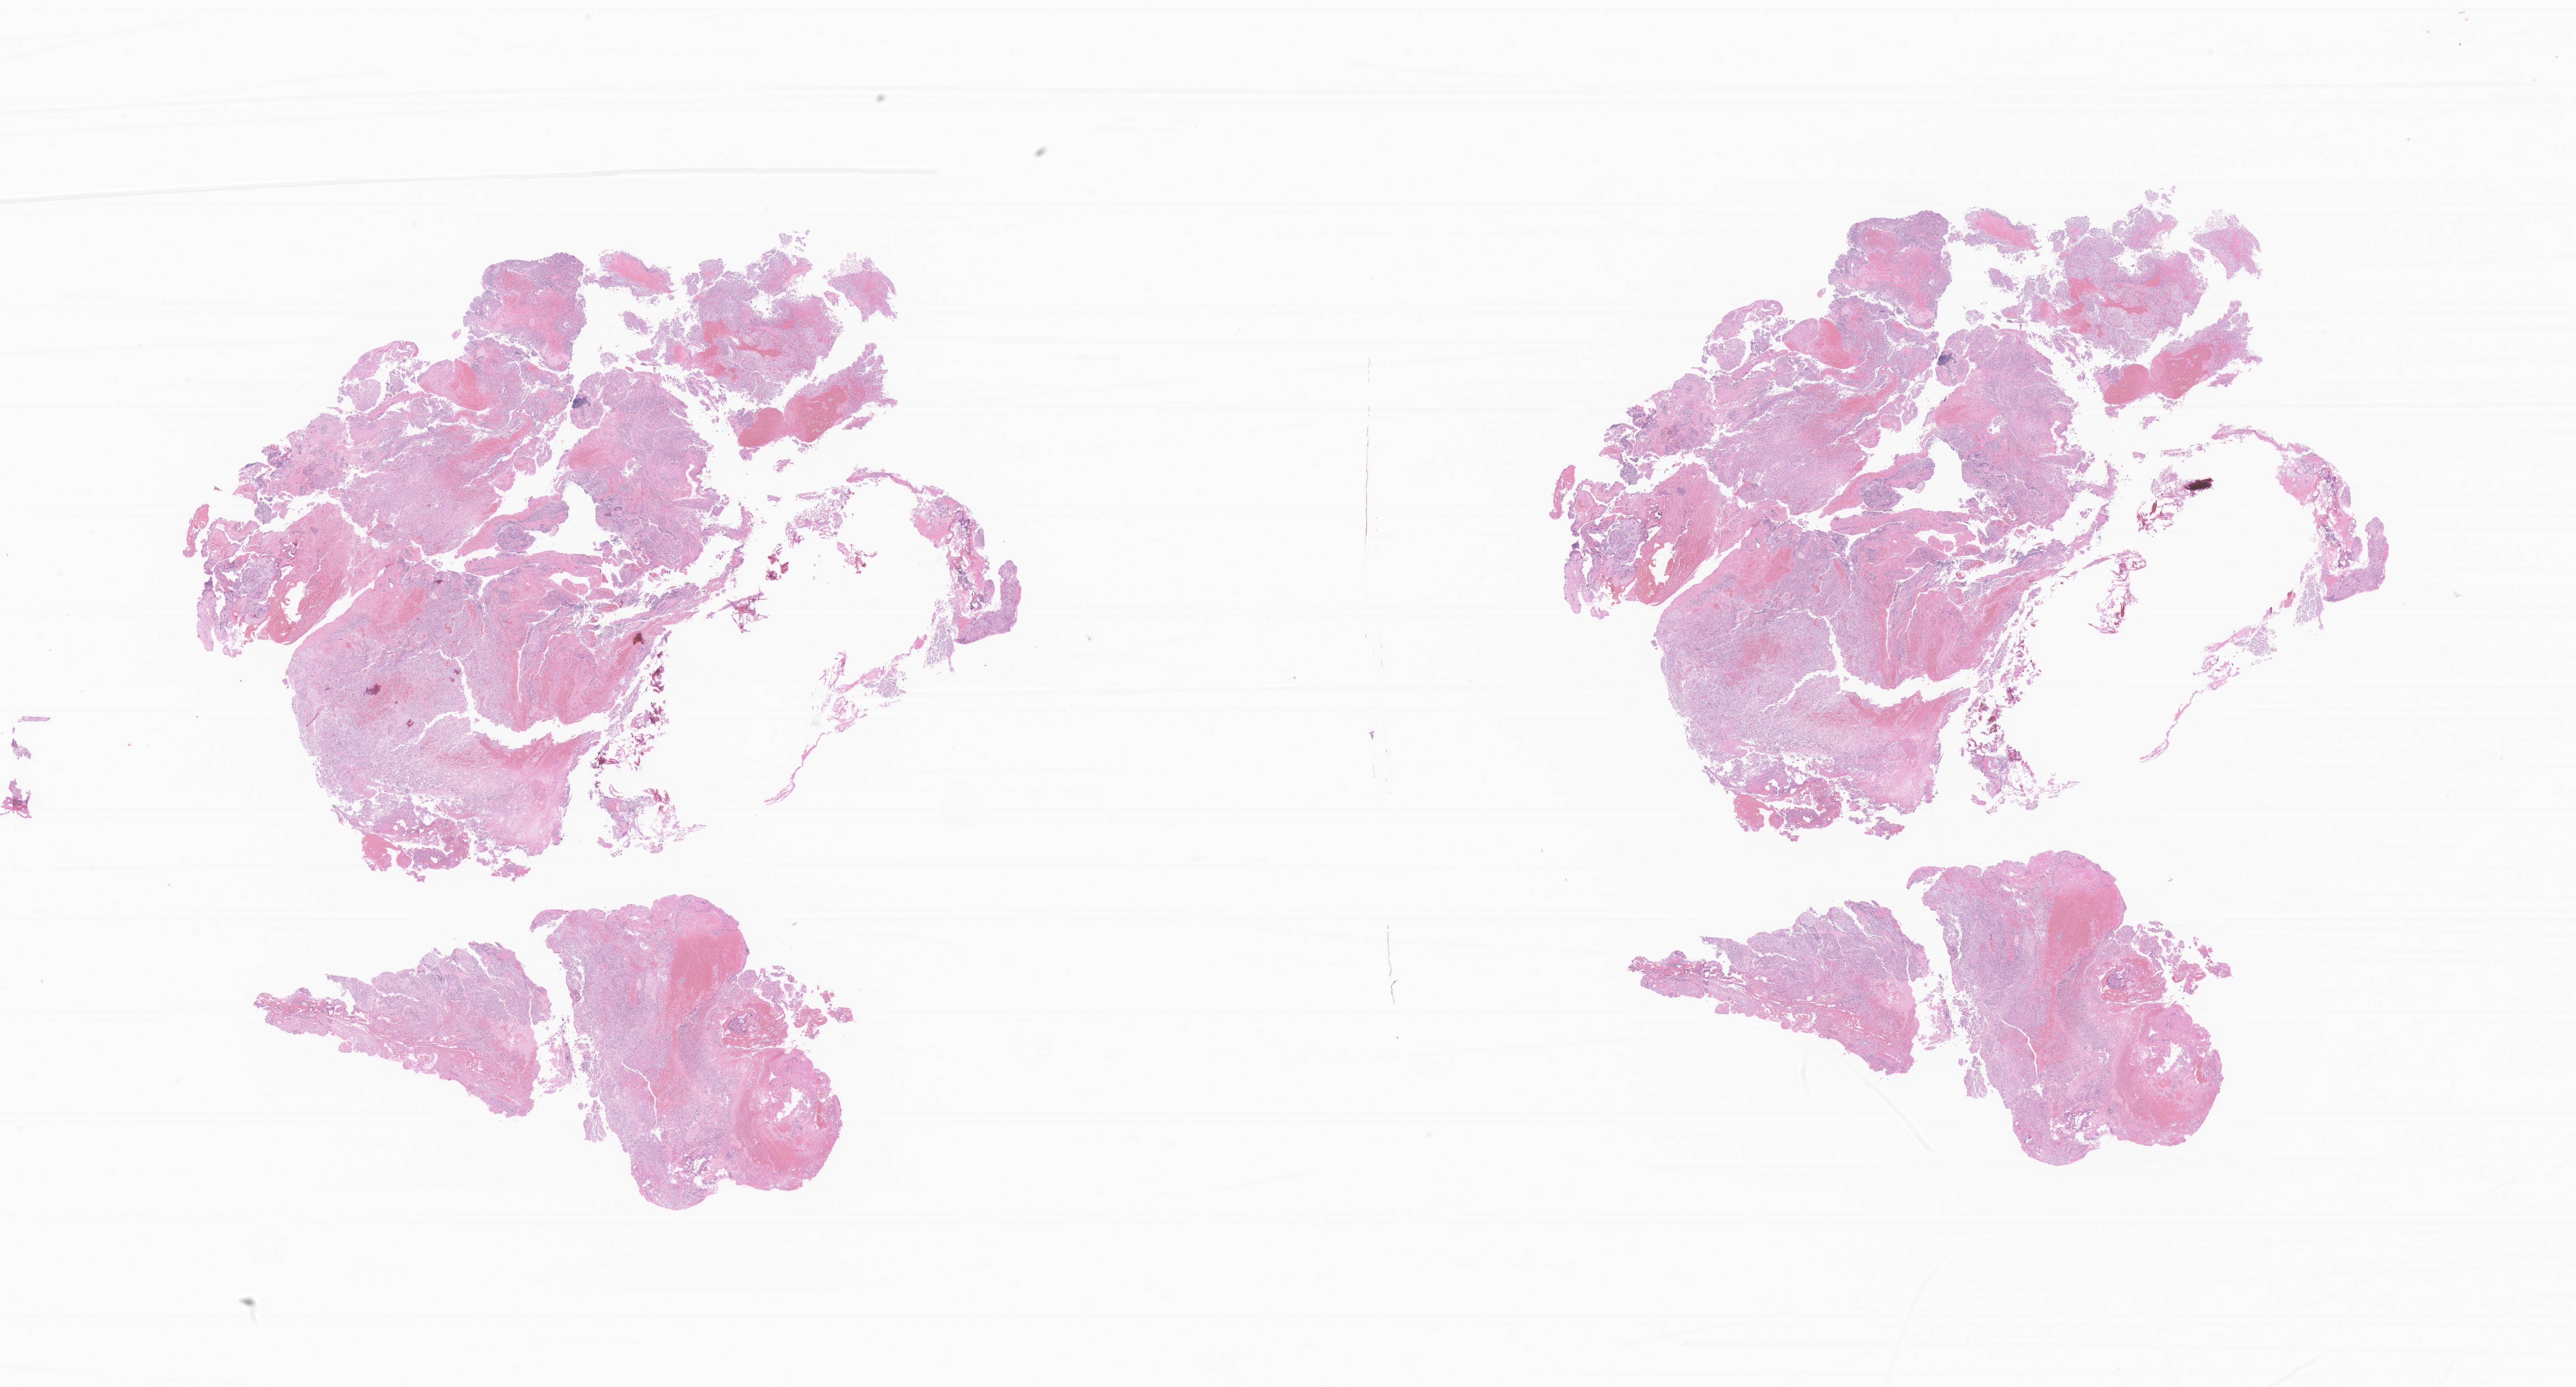
Whole-slide image, hematoxylin and eosin (H&E) stain of tumor tissue from the brain, low-resolution overview of the scanned area, about 27.2 x 14.7 mm; formalin-fixed paraffin-embedded section. Patient: female, age 50 months (4 years 2 months).
Diagnosis: Atypical teratoid/rhabdoid tumor.